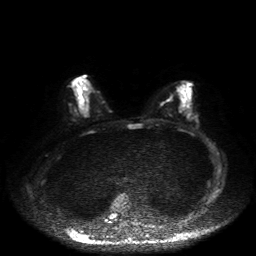
Breast MRI, one axial slice; slice 26 of 50 in the series (ordered by position); diffusion-weighted series; image 2 of 4 stored at this slice position (different b-values; order by instance number); 1.5 T; 4 mm slice thickness; 256 × 256 image matrix, field of view 360 × 360 mm. Female patient.
Outlined on this slice (outlined manually by an expert reader):
- tumour on diffusion-weighted imaging: bounding box <80,106,85,113> (left, top, right, bottom; pixels)